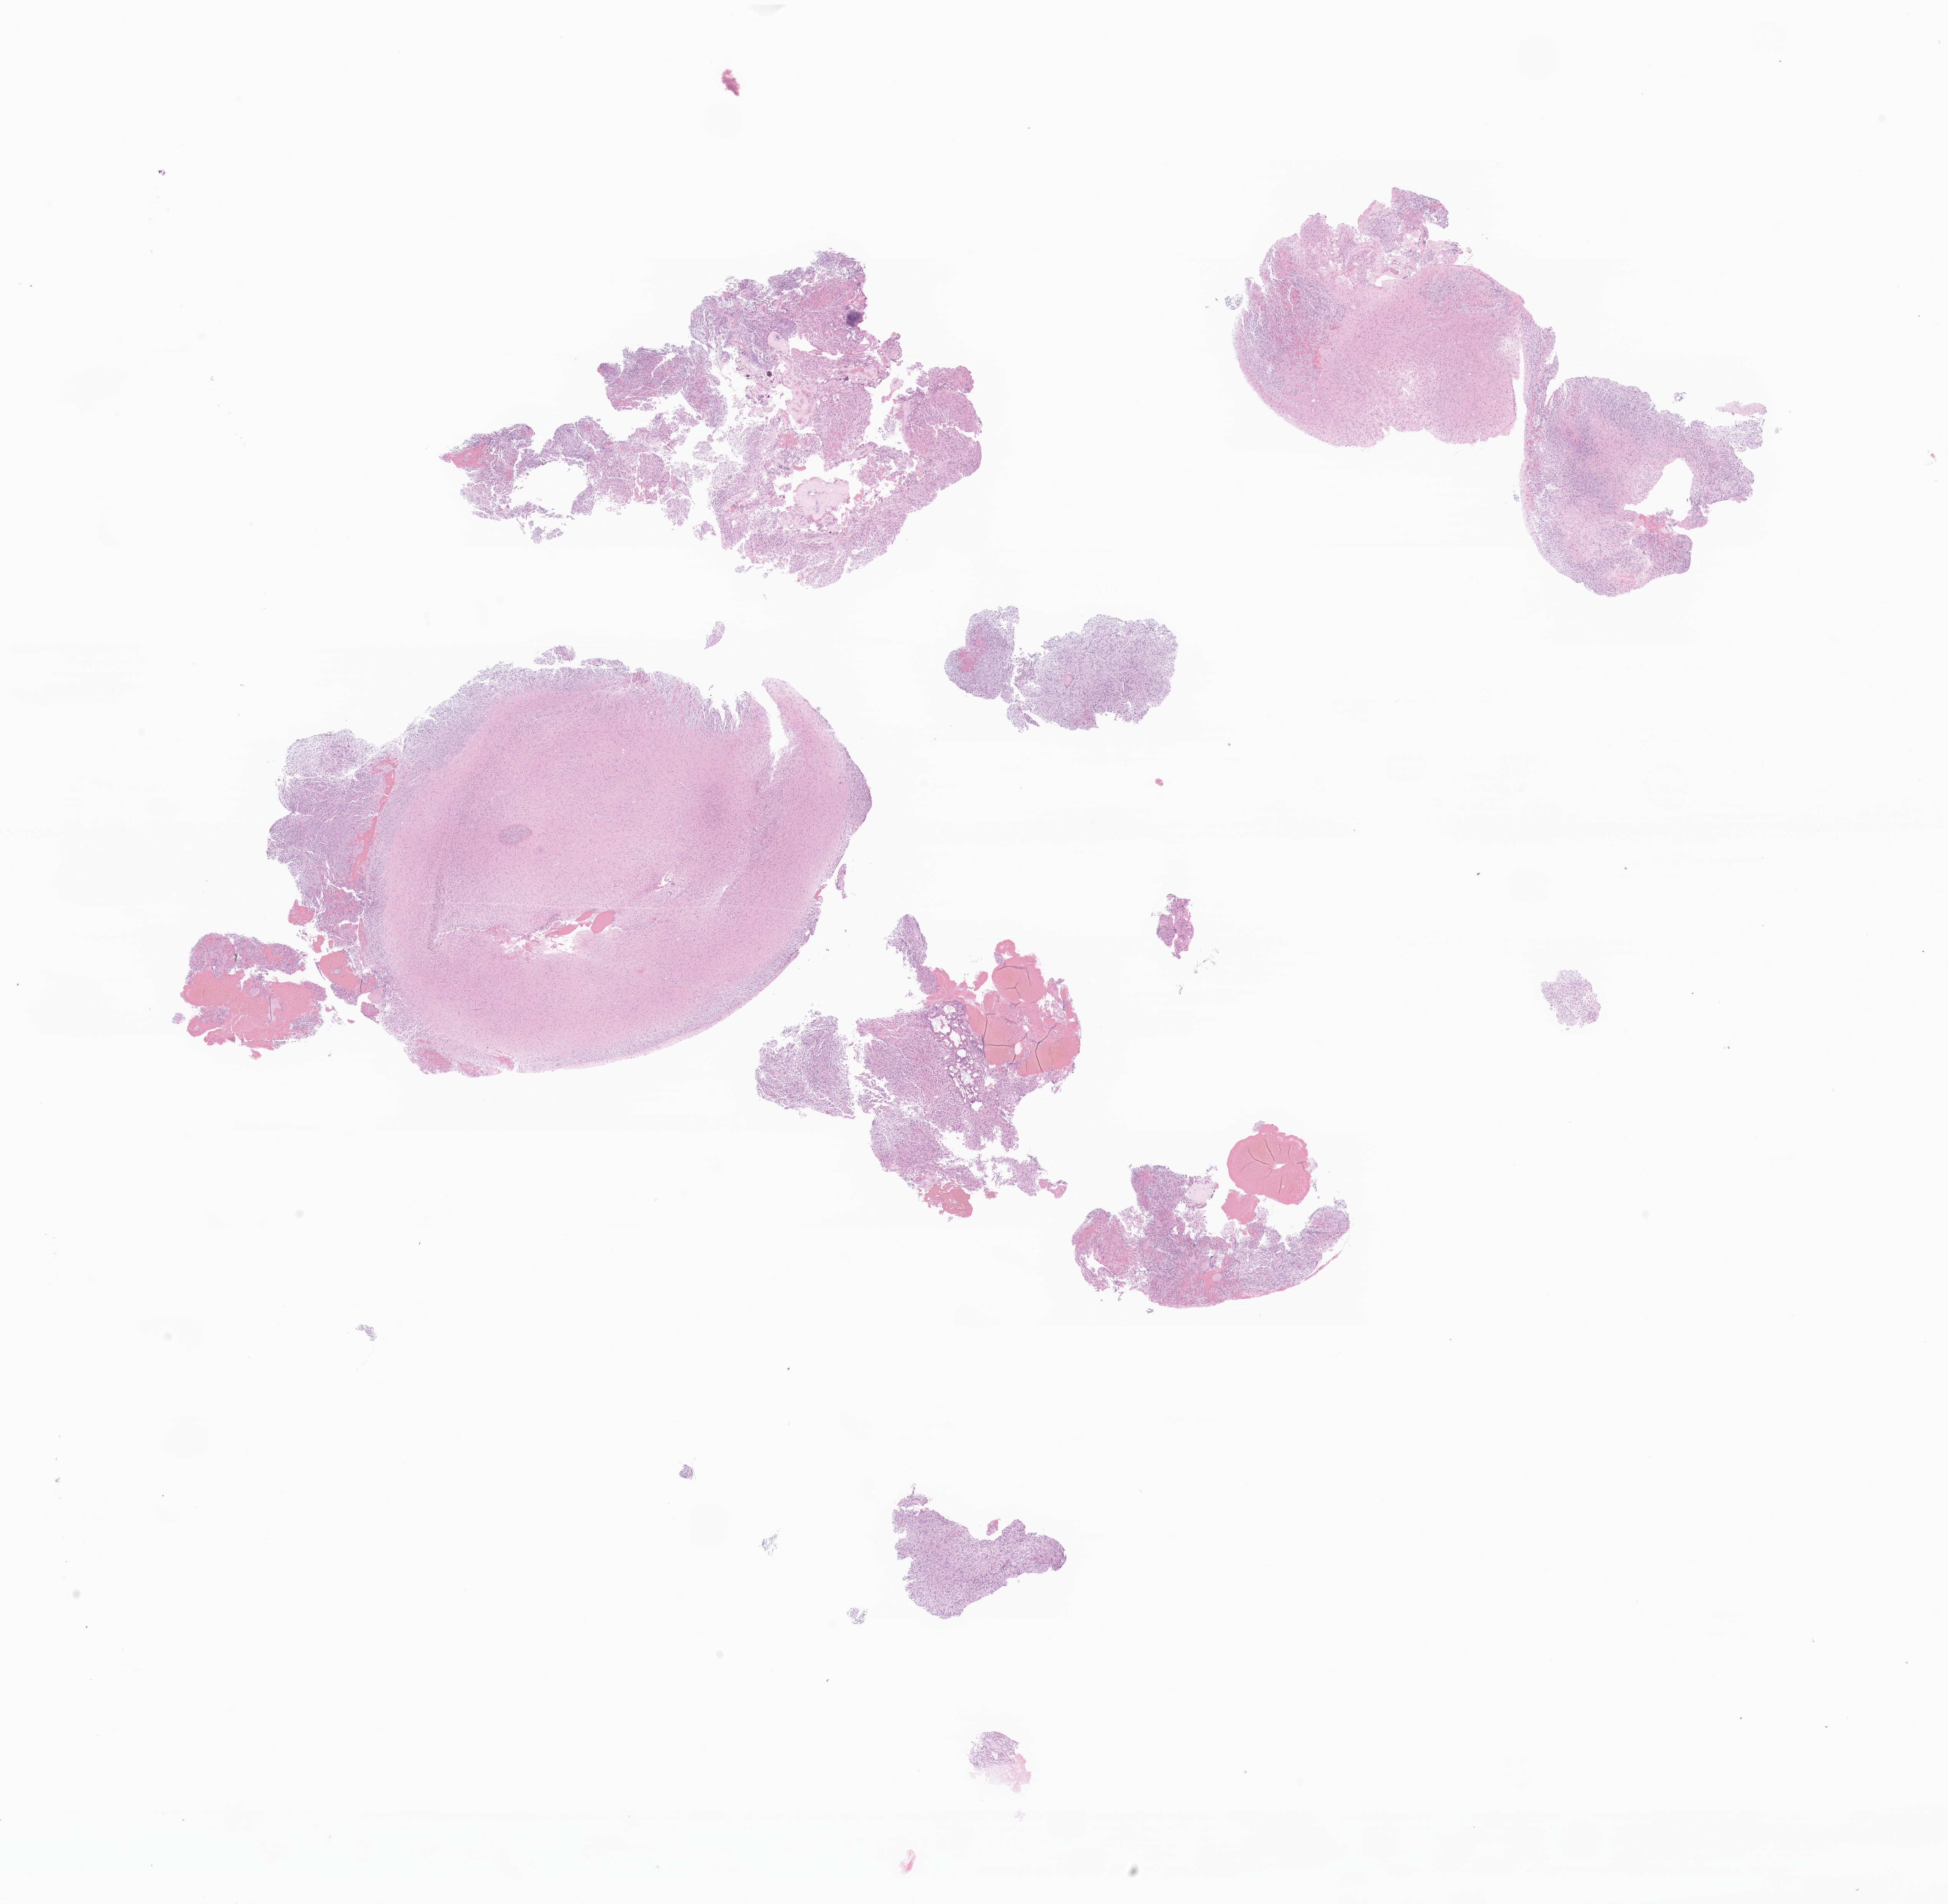
Whole-slide image, hematoxylin and eosin (H&E) stain of tumor tissue from the pineal gland, low-resolution overview of the scanned area, about 21.4 x 20.9 mm, formalin-fixed, paraffin-embedded (FFPE) tissue. Female patient, age 132 months (11 years).
Diagnosis: Neoplasm, malignant.